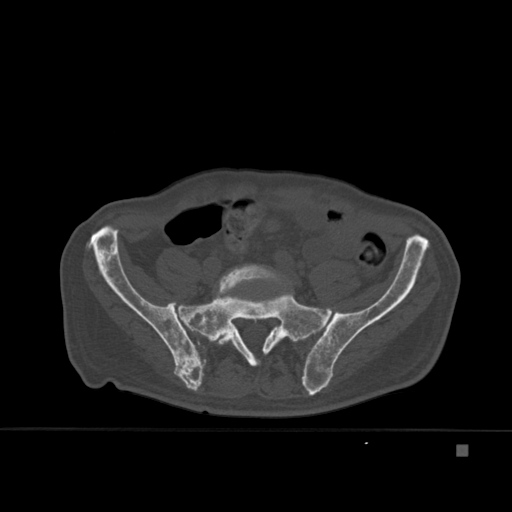
CT including the spine, one axial slice; slice 91 of 451 in the series (ordered by position); bone window (W 1800 / L 400 HU); 1.5 mm slice thickness; 512 × 512 image matrix, field of view 378 × 378 mm. Male patient, age 75 years. From the clinical record (not read from this slice): primary cancer: prostate.
Outlined on this slice (semi-automatically segmented with operator editing):
- L5 vertebra: box from (x=217, y=264) to (x=282, y=354) px